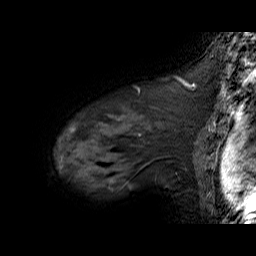
Breast MRI (dynamic contrast-enhanced), one sagittal slice. Slice 53 of 60 in the series (ordered by position). Dynamic contrast-enhanced series, time point 2 of 6 at this slice position (early post-contrast). 1.5 T. TE 6.3 ms, TR 32.9 ms. 4 mm slice thickness. 256 × 256 image matrix, field of view 200 × 200 mm. Female patient. Case-level facts recorded for this patient, not image findings: setting: breast cancer imaged before/during neoadjuvant chemotherapy; receptor status: HER2-positive.
Annotated regions visible in this slice (semi-automatically segmented with operator editing):
- analysis volume of interest (the breast-tissue region the enhancement analysis was run in; not a lesion): bounding box [x1, y1, x2, y2] px = [57, 92, 195, 174]
- tumour enhancement mask (voxels above the 100 % enhancement threshold inside the analysis volume of interest): [71, 127, 75, 132]